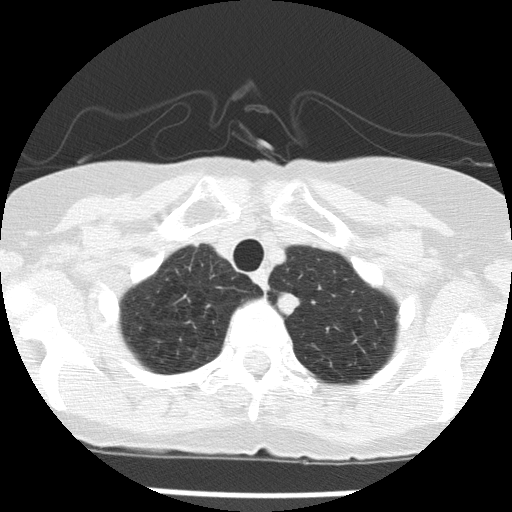
Chest CT (low-dose screening protocol), one axial image. First (baseline) screen. Lung window (W 1500 / L -600 HU). 2 mm slice thickness. Lung (sharp) reconstruction kernel (FC51). Slice 18 of 143 in the series. 512 × 512 image matrix, field of view 276 × 276 mm. Female participant, aged 74 years at enrolment. Former smoker at enrolment.
Lesion marked by an expert reader, bounding box [x1, y1, x2, y2] px = [270, 289, 306, 318]. The screening reader recorded 2 non-calcified nodules or masses ≥4 mm on this exam (left lower lobe, left upper lobe); which of them this box marks is not recorded.